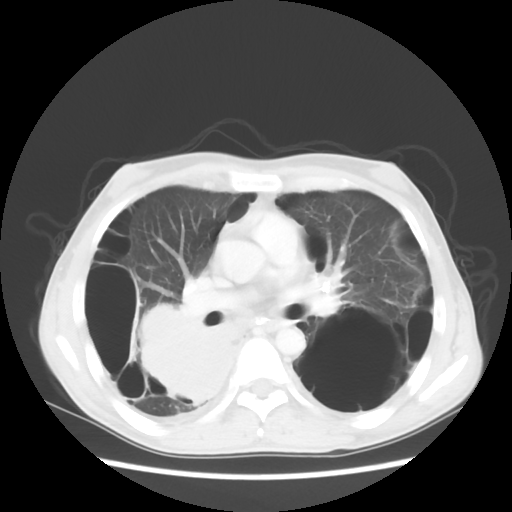
Chest CT, one axial slice. Slice 30 of 56 in the series (ordered by position). Reconstruction kernel STANDARD. 140 kVp. Lung window (W 1500 / L -600 HU). 5 mm slice thickness. 512 × 512 image matrix, field of view 351 × 351 mm. Patient: male, 41 years. From the clinical record (not read from this slice): clinical TNM (as recorded): T4 N0 M1a; histopathological grade: G3.
Structures marked on this image (rectangle marked by the reading radiologist):
- lung tumour (recorded histology: large cell carcinoma): box from (x=129, y=295) to (x=246, y=403) px